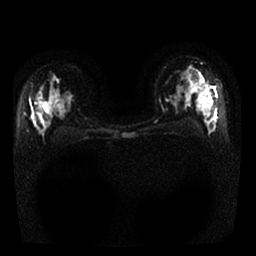
Breast MRI, one axial slice. Slice 17 of 25 in the series (ordered by position). Diffusion-weighted series; image 2 of 4 stored at this slice position (different b-values; order by instance number). 1.5 T. 256 × 256 image matrix, field of view 320 × 320 mm. Female patient.
Structures marked on this image (manually delineated by an expert):
- tumour on diffusion-weighted imaging: box from (x=194, y=75) to (x=212, y=97) px